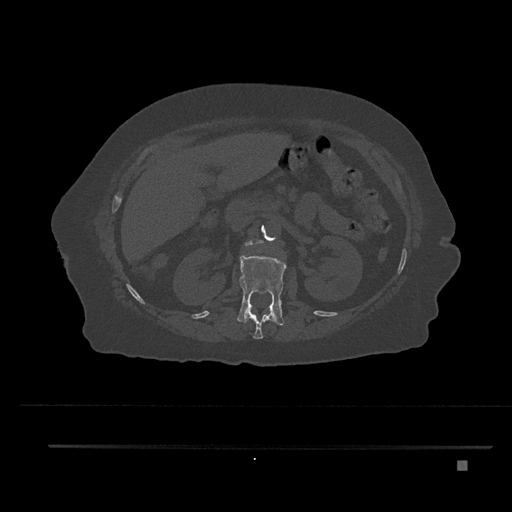
CT including the spine, one axial slice. Position 229 of 797 along the scan axis. Bone window (W 1800 / L 400 HU). 512 × 512 image matrix. Patient: female, 76 years. Case-level facts recorded for this patient, not image findings: primary cancer: lung; vertebrae with lytic lesions (as recorded): T11, L3.
Structures marked on this image (semi-automatically segmented with operator editing):
- L1 vertebra: bounding box (x1, y1, x2, y2) in pixels: (237, 253, 286, 326)
- L2 vertebra: (245, 239, 260, 247)
- T12 vertebra: (244, 306, 277, 339)